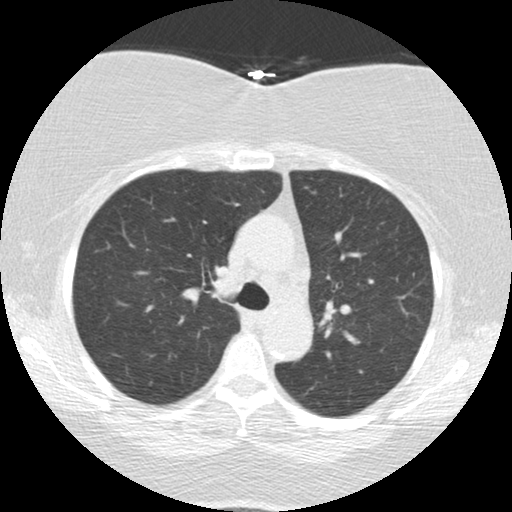
Low-dose screening chest CT, one axial slice; position 94 of 136 along the scan axis; reconstruction kernel STANDARD; 120 kVp; lung window (W 1500 / L -600 HU); 512 × 512 image matrix, field of view 309 × 309 mm.
Outlined on this slice (expert manual segmentation):
- lesion 1 (tumor): bounding box [x1, y1, x2, y2] px = [213, 265, 239, 298]